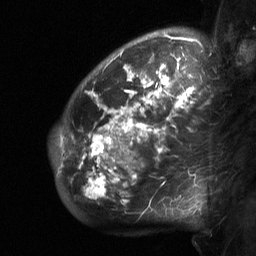
Breast MRI (dynamic contrast-enhanced), one sagittal slice. Slice 50 of 64 in the series (ordered by position). Dynamic contrast-enhanced study with each time point stored as its own series, time point 2 of 3 at this slice position (early post-contrast, ordered by acquisition time). 1.5 T. TE 4.8 ms, TR 27 ms. 256 × 256 image matrix, field of view 200 × 200 mm. Patient: female, 50 years. Case-level facts recorded for this patient, not image findings: setting: breast cancer imaged before/during neoadjuvant chemotherapy; receptor status: HER2-positive.
Annotated regions visible in this slice (semi-automatic segmentation, software-assisted and operator-edited):
- analysis volume of interest (the breast-tissue region the enhancement analysis was run in; not a lesion): bounding box [x1, y1, x2, y2] px = [52, 62, 218, 222]
- tumour enhancement mask (voxels above the 90 % enhancement threshold inside the analysis volume of interest): [79, 63, 195, 202]